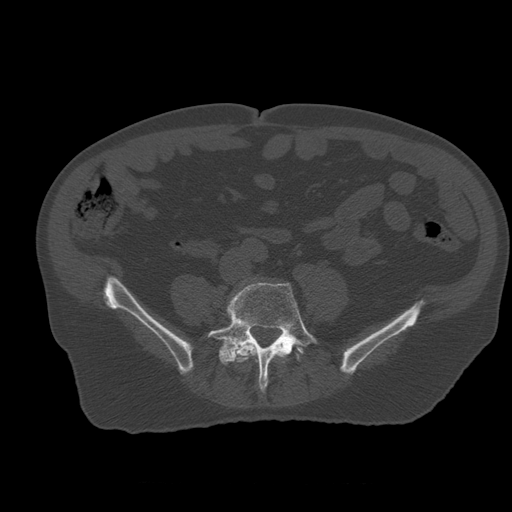
CT including the spine, one axial slice; position 146 of 399 along the scan axis; reconstruction kernel STANDARD; 120 kVp; bone window (W 1800 / L 400 HU); 1.25 mm slice thickness; 512 × 512 image matrix, field of view 407 × 407 mm. Patient age 73 years. From the clinical record (not read from this slice): primary cancer: prostate.
Structures marked on this image (semi-automatically segmented with operator editing):
- L4 vertebra: bounding box (x1, y1, x2, y2) in pixels: (232, 343, 259, 363)
- L5 vertebra: (208, 283, 318, 391)